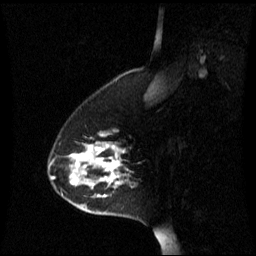
Breast MRI (dynamic contrast-enhanced), one sagittal slice; slice 16 of 60 in the series (ordered by position); dynamic contrast-enhanced series, image 2 of 3 at this slice position (ordered by acquisition); 1.5 T; TE 4.2 ms, TR 8.4 ms; 2.2 mm slice thickness; 256 × 256 image matrix, field of view 240 × 240 mm. Patient: female, 45 years. Case-level facts recorded for this patient, not image findings: setting: breast cancer imaged before/during neoadjuvant chemotherapy; receptor status: HR-positive, HER2-negative.
Annotated regions visible in this slice (semi-automatically segmented with operator editing):
- analysis volume of interest (the breast-tissue region the enhancement analysis was run in; not a lesion): bounding box (x1, y1, x2, y2) in pixels: (48, 132, 133, 219)
- tumour enhancement mask (voxels above the 70 % enhancement threshold inside the analysis volume of interest): (72, 134, 123, 197)